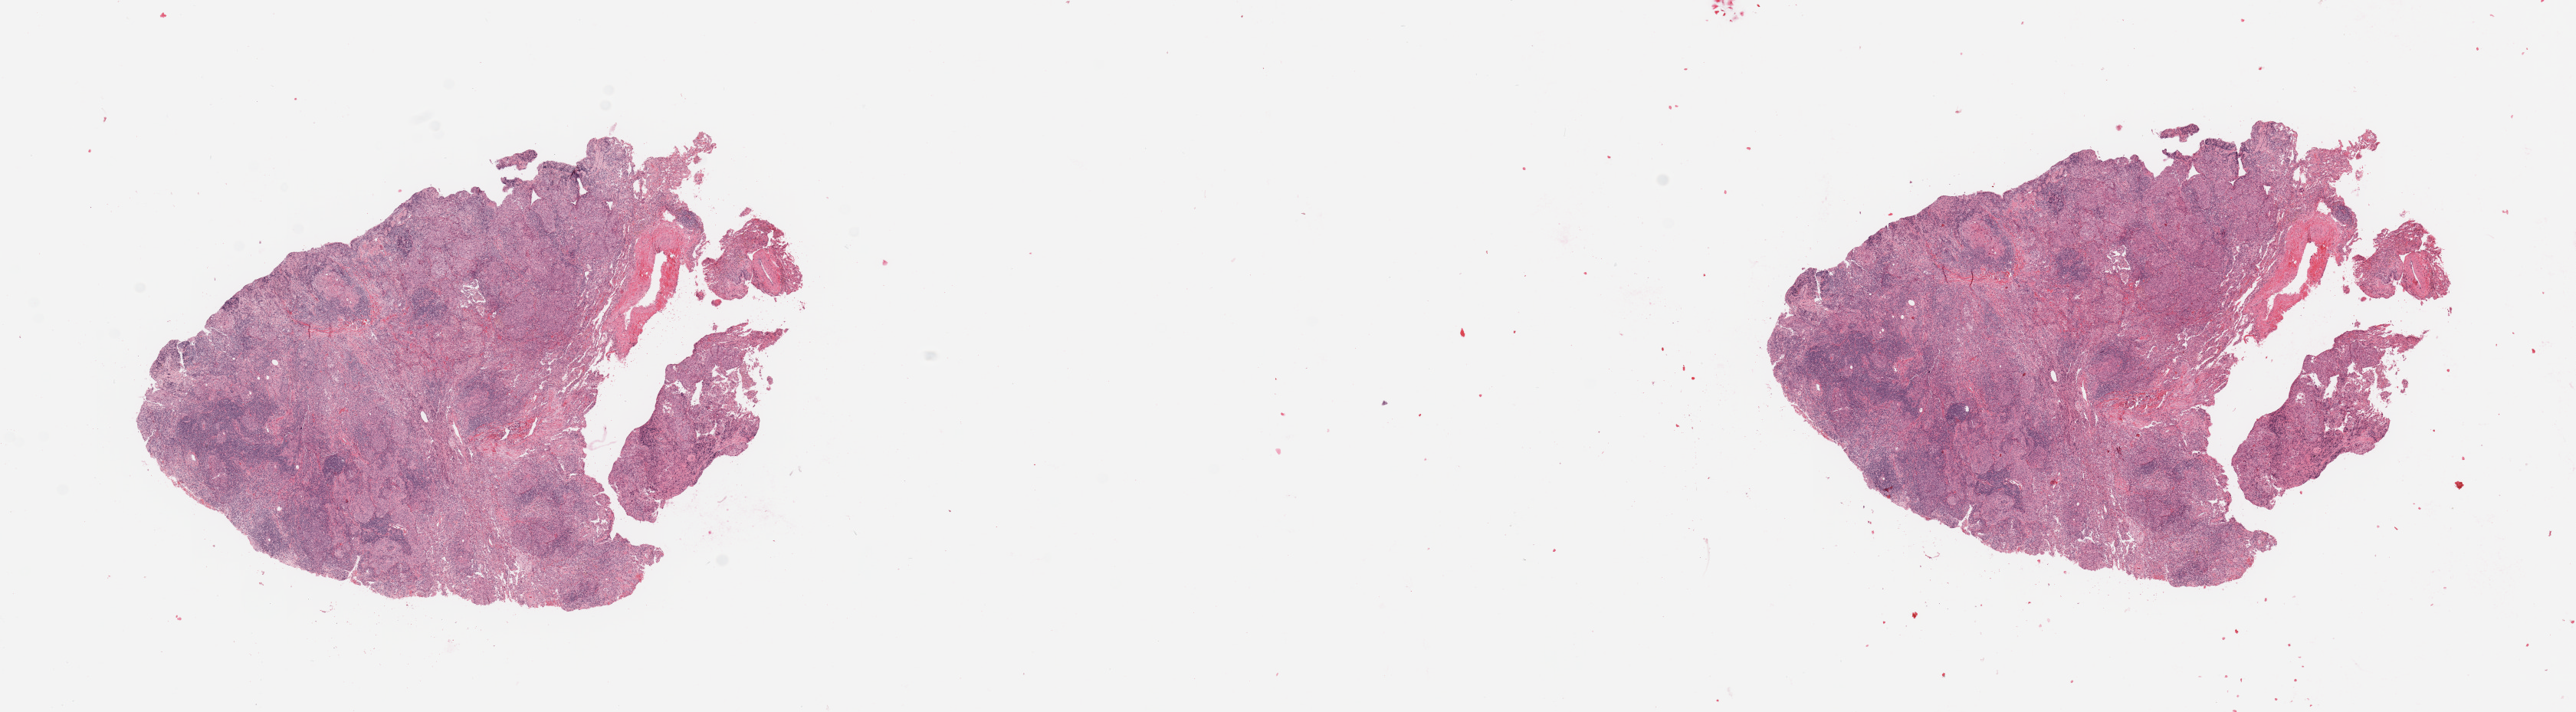
H&E whole-slide image, shown as a low-resolution overview of the whole scanned area (about 26.6 x 7.3 mm), tumour tissue sample, sampled site: lung. 77-year-old female patient. Histologic grade: G3 (poorly differentiated). Slide review estimates, as recorded: tumour nuclei 65%, necrosis 5%.
• primary tumour site (as recorded): right lower lobe
• AJCC pathologic stage: IIA
• histologic diagnosis: Squamous cell carcinoma, NOS